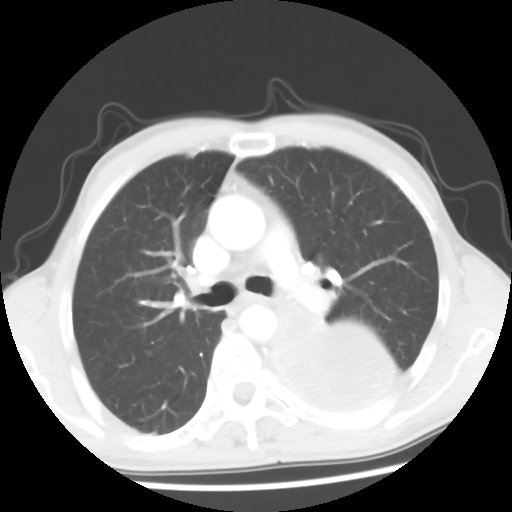
Chest CT, one axial slice; position 36 of 56 along the scan axis; 120 kVp; lung window (W 1500 / L -600 HU); 5 mm slice thickness; 512 × 512 image matrix. Male patient, age 60 years. Case-level facts recorded for this patient, not image findings: clinical TNM (as recorded): T4 N0 M0.
Outlined on this slice (bounding box drawn by a radiologist):
- lung tumour (recorded histology: squamous cell carcinoma): bounding box <251,290,422,433> (left, top, right, bottom; pixels)